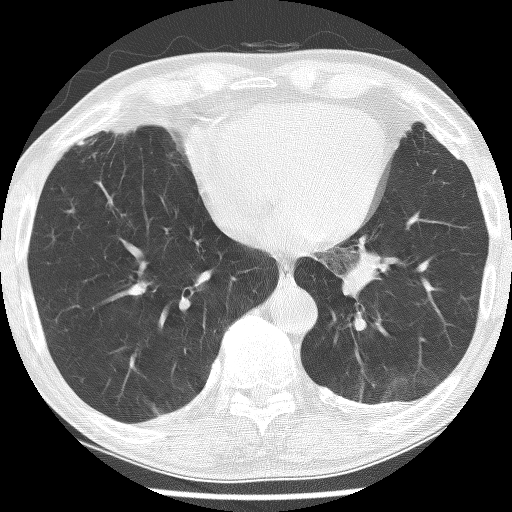
Low-dose screening chest CT, one axial slice. Reconstruction kernel BONE. 120 kVp. Lung window (W 1500 / L -600 HU). 2.5 mm slice thickness. 512 × 512 image matrix, field of view 320 × 320 mm.
Annotated regions visible in this slice (expert manual segmentation):
- lesion 1 (tumor, lower lobe of left lung): box from (x=340, y=253) to (x=380, y=301) px